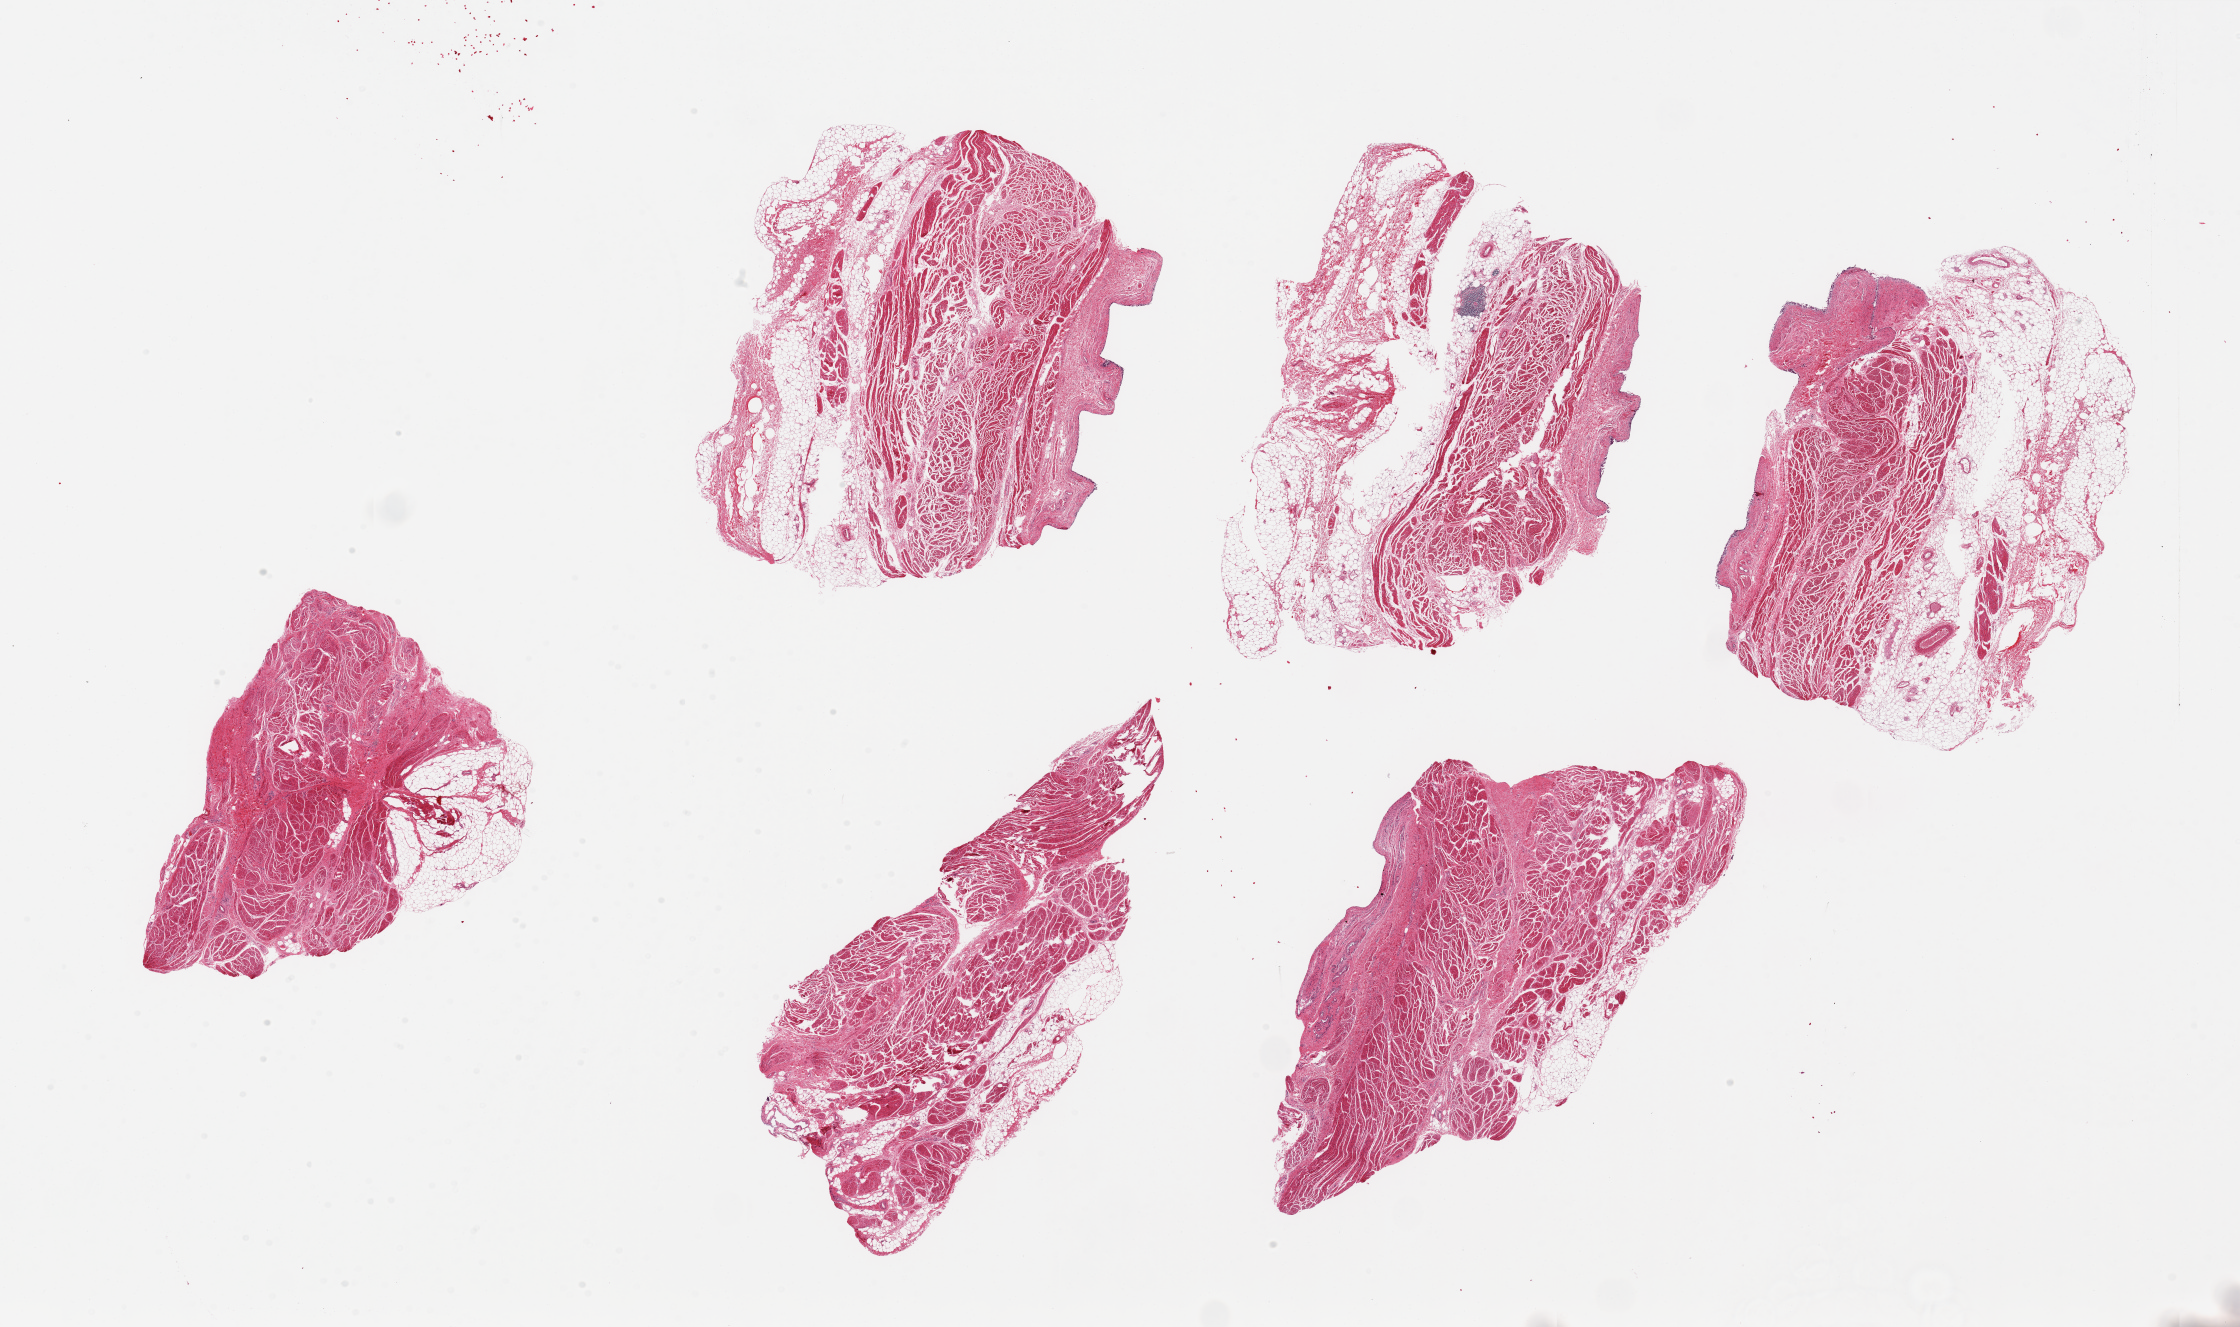
Digitized haematoxylin and eosin-stained section, shown as a low-resolution overview of the whole scanned area (about 35.4 x 21.0 mm, from a 20x scan); PAXgene-fixed paraffin-embedded (PFPE) section; sampled site (target tissue): urinary bladder; tissue donor sample. Donor sex: male.
• review note (as recorded): 6 pieces up to 9x5.8 mm; mucosa largely sloughed, shows cassette grid compression artifact; muscle only slightly autolyzed